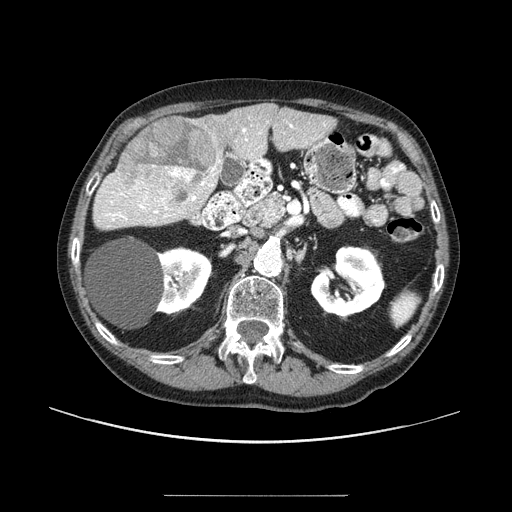
Contrast-enhanced abdominal CT (liver protocol), one axial slice; position 43 of 91 along the scan axis; 100 kVp; one of 2 acquisitions stored at this slice position; soft-tissue window (W 400 / L 40 HU); 2.5 mm slice thickness; 512 × 512 image matrix, field of view 400 × 400 mm. Case-level facts recorded for this patient, not image findings: diagnosis: hepatocellular carcinoma (patient treated with transarterial chemoembolisation; whether this scan precedes or follows treatment is not stated here); TNM stage (as recorded): Stage-I; Child-Pugh class: A.
Annotated regions visible in this slice (semi-automatically segmented with operator editing):
- liver parenchyma outside the tumour (the mass and vessels are separate outlines, so this box may not span the whole liver): bounding box <116,104,336,218> (left, top, right, bottom; pixels)
- mass: <119,117,217,209>
- liver vessels: <125,124,293,197>